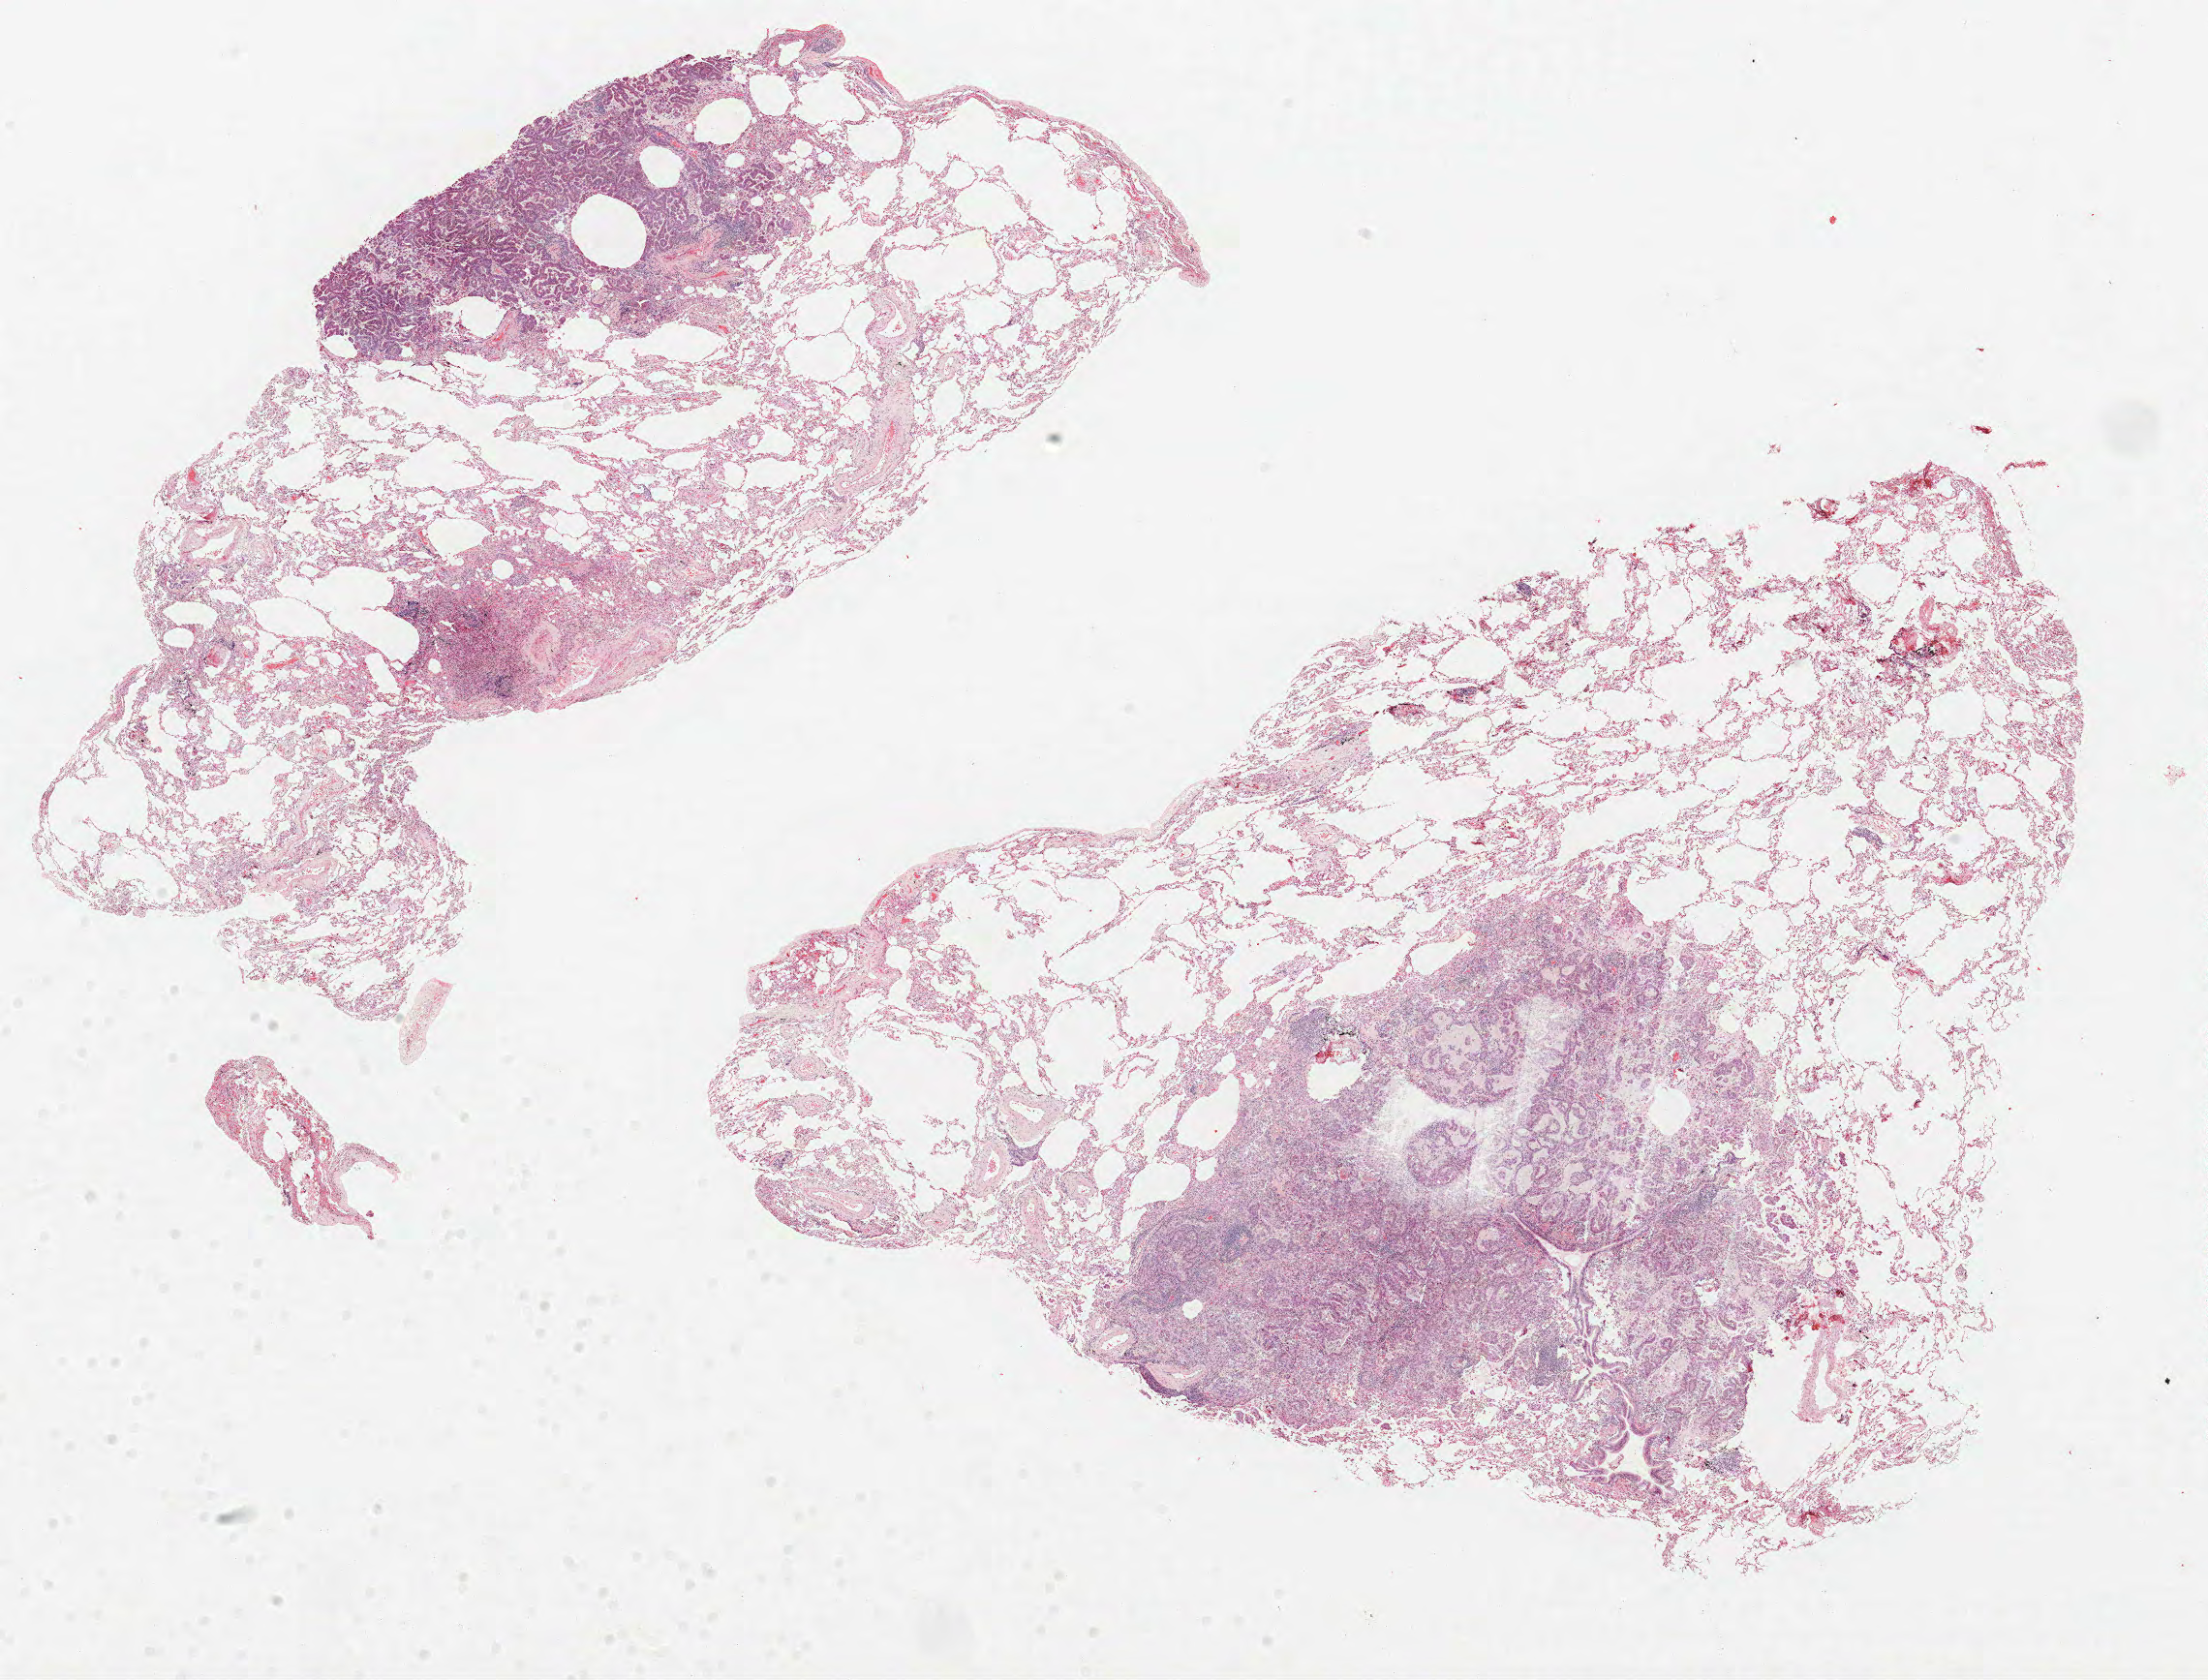
H&E whole-slide image, low-resolution overview of the scanned area, about 18.2 x 13.9 mm, formalin-fixed paraffin-embedded (FFPE) section, lung tissue. Female, age 66 at enrolment. Current smoker at enrolment. Grade: moderately differentiated (G2).
Primary tumour location (clinical record): right lower lobe. Stage (AJCC 6th edition): IIA. Tumour size (pathology): 11 mm. Participant's lung-cancer diagnosis: Adenocarcinoma, NOS.